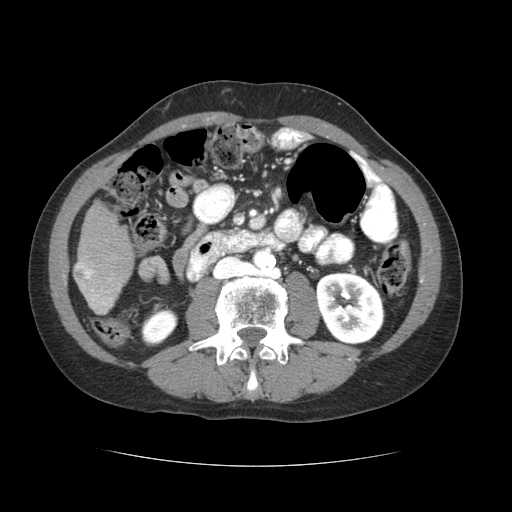
Contrast-enhanced abdominal CT (liver protocol), one axial slice. Slice 13 of 69 in the series (ordered by position). Reconstruction kernel STANDARD. 120 kVp. Soft-tissue window (W 400 / L 40 HU). 2.5 mm slice thickness. 512 × 512 image matrix, field of view 360 × 360 mm. Case-level facts recorded for this patient, not image findings: diagnosis: hepatocellular carcinoma (patient treated with transarterial chemoembolisation; whether this scan precedes or follows treatment is not stated here); TNM stage (as recorded): Stage-II; Child-Pugh class: B; tumour nodularity: multinodular; tumour size: 2.6 cm.
Structures marked on this image (semi-automatic segmentation, software-assisted and operator-edited):
- liver parenchyma outside the tumour (the mass and vessels are separate outlines, so this box may not span the whole liver): box from (x=74, y=202) to (x=134, y=314) px
- liver vessels: (x=76, y=262)–(x=112, y=311)